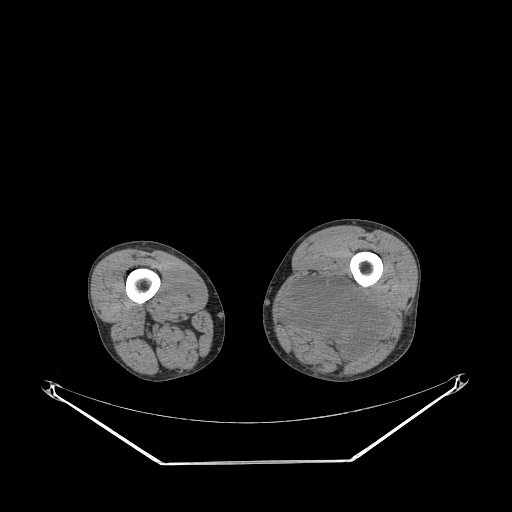
CT of an extremity soft-tissue mass (from a PET/CT study), one axial slice; reconstruction kernel STANDARD; 140 kVp; soft-tissue window (W 400 / L 40 HU); 3.75 mm slice thickness; 512 × 512 image matrix, field of view 500 × 500 mm. Male patient. Case-level facts recorded for this patient, not image findings: histological type: undifferentiated pleomorphic liposarcoma; grade: high; site of the primary tumour: left thigh.
Annotated regions visible in this slice (expert contour drawn on MRI and transferred to this co-registered scan by the dataset authors):
- gross tumour volume including surrounding oedema: bounding box (x1, y1, x2, y2) in pixels: (285, 274, 385, 359)
- gross tumour volume (mass): (285, 279, 385, 359)